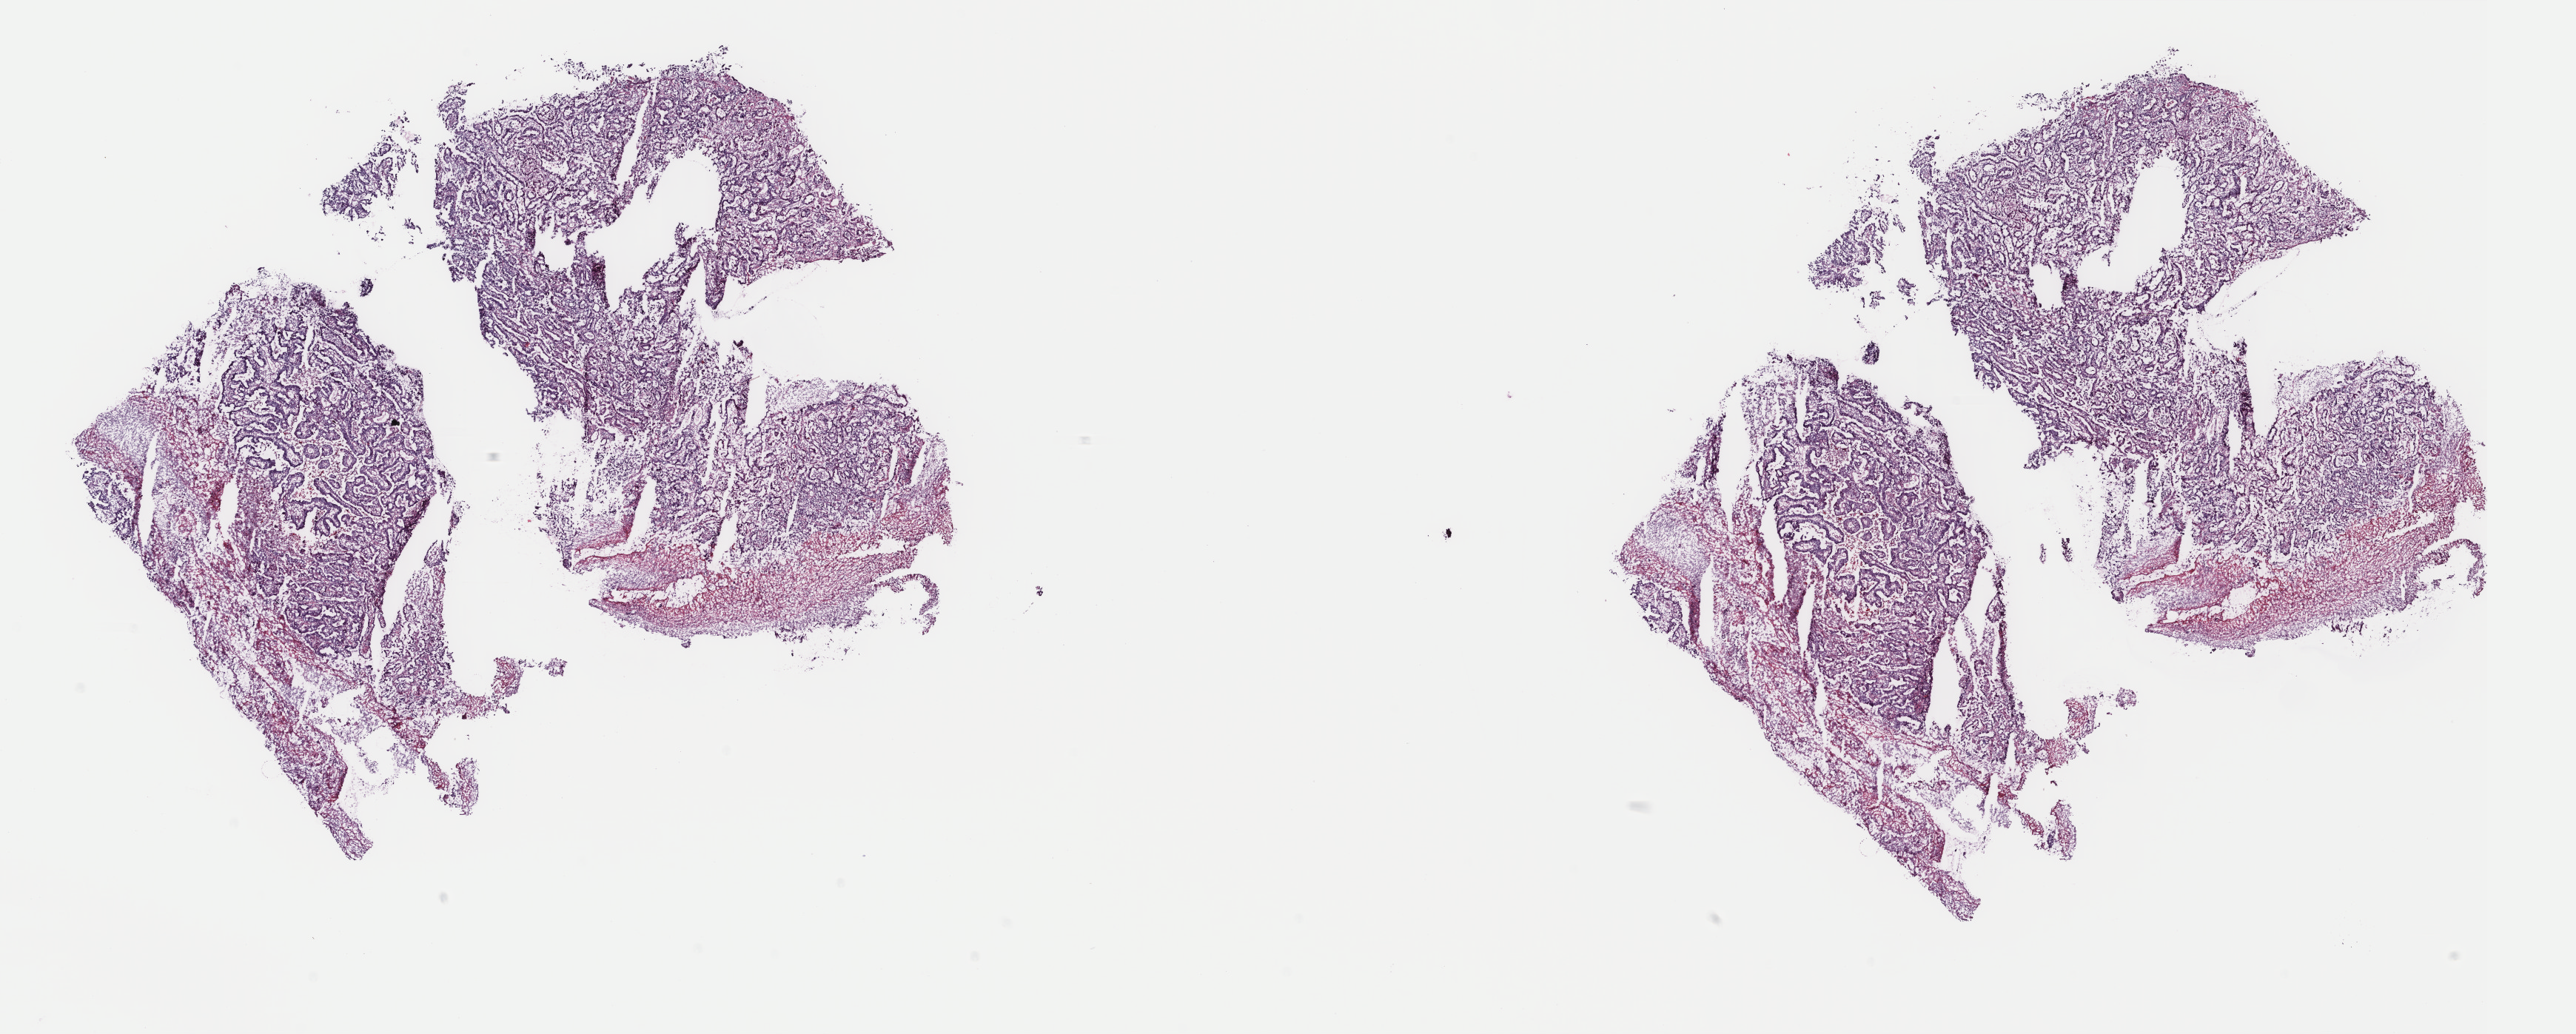
Whole-slide histology image, H&E, low-resolution overview of the scanned area, about 27.6 x 11.1 mm (slide scanned at 40x). Frozen section. Primary tumour sample from the stomach. Male patient; age at initial diagnosis 45 years. Histologic grade: G2 (moderately differentiated). Pathologist review of this section (percent, as recorded): tumour cells 83%, tumour nuclei 70%, normal cells 0%, stromal cells 0%, necrosis 17%. Infiltration values recorded for this section: lymphocyte infiltration 5%, monocyte infiltration 5%, neutrophil infiltration 5%.
• AJCC pathologic stage: I (7th edition)
• lymph nodes positive (case pathology): 0 of 13 examined
• histologic diagnosis: Adenocarcinoma, NOS (cardia, NOS)